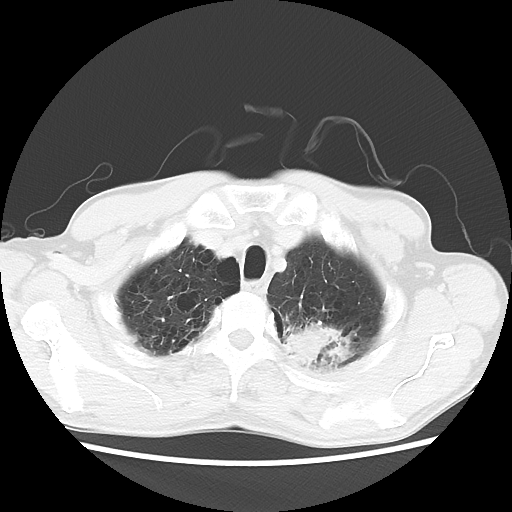
Chest CT, one axial slice; slice 56 of 64 in the series (ordered by position); reconstruction kernel LUNG; 120 kVp; lung window (W 1500 / L -600 HU); 5 mm slice thickness; 512 × 512 image matrix, field of view 346 × 346 mm. Male patient, age 63 years. Case-level facts recorded for this patient, not image findings: clinical TNM (as recorded): T2 N0 M0.
Annotated regions visible in this slice (bounding box drawn by a radiologist):
- lung tumour (recorded histology: adenocarcinoma): bounding box (x1, y1, x2, y2) in pixels: (283, 318, 357, 378)